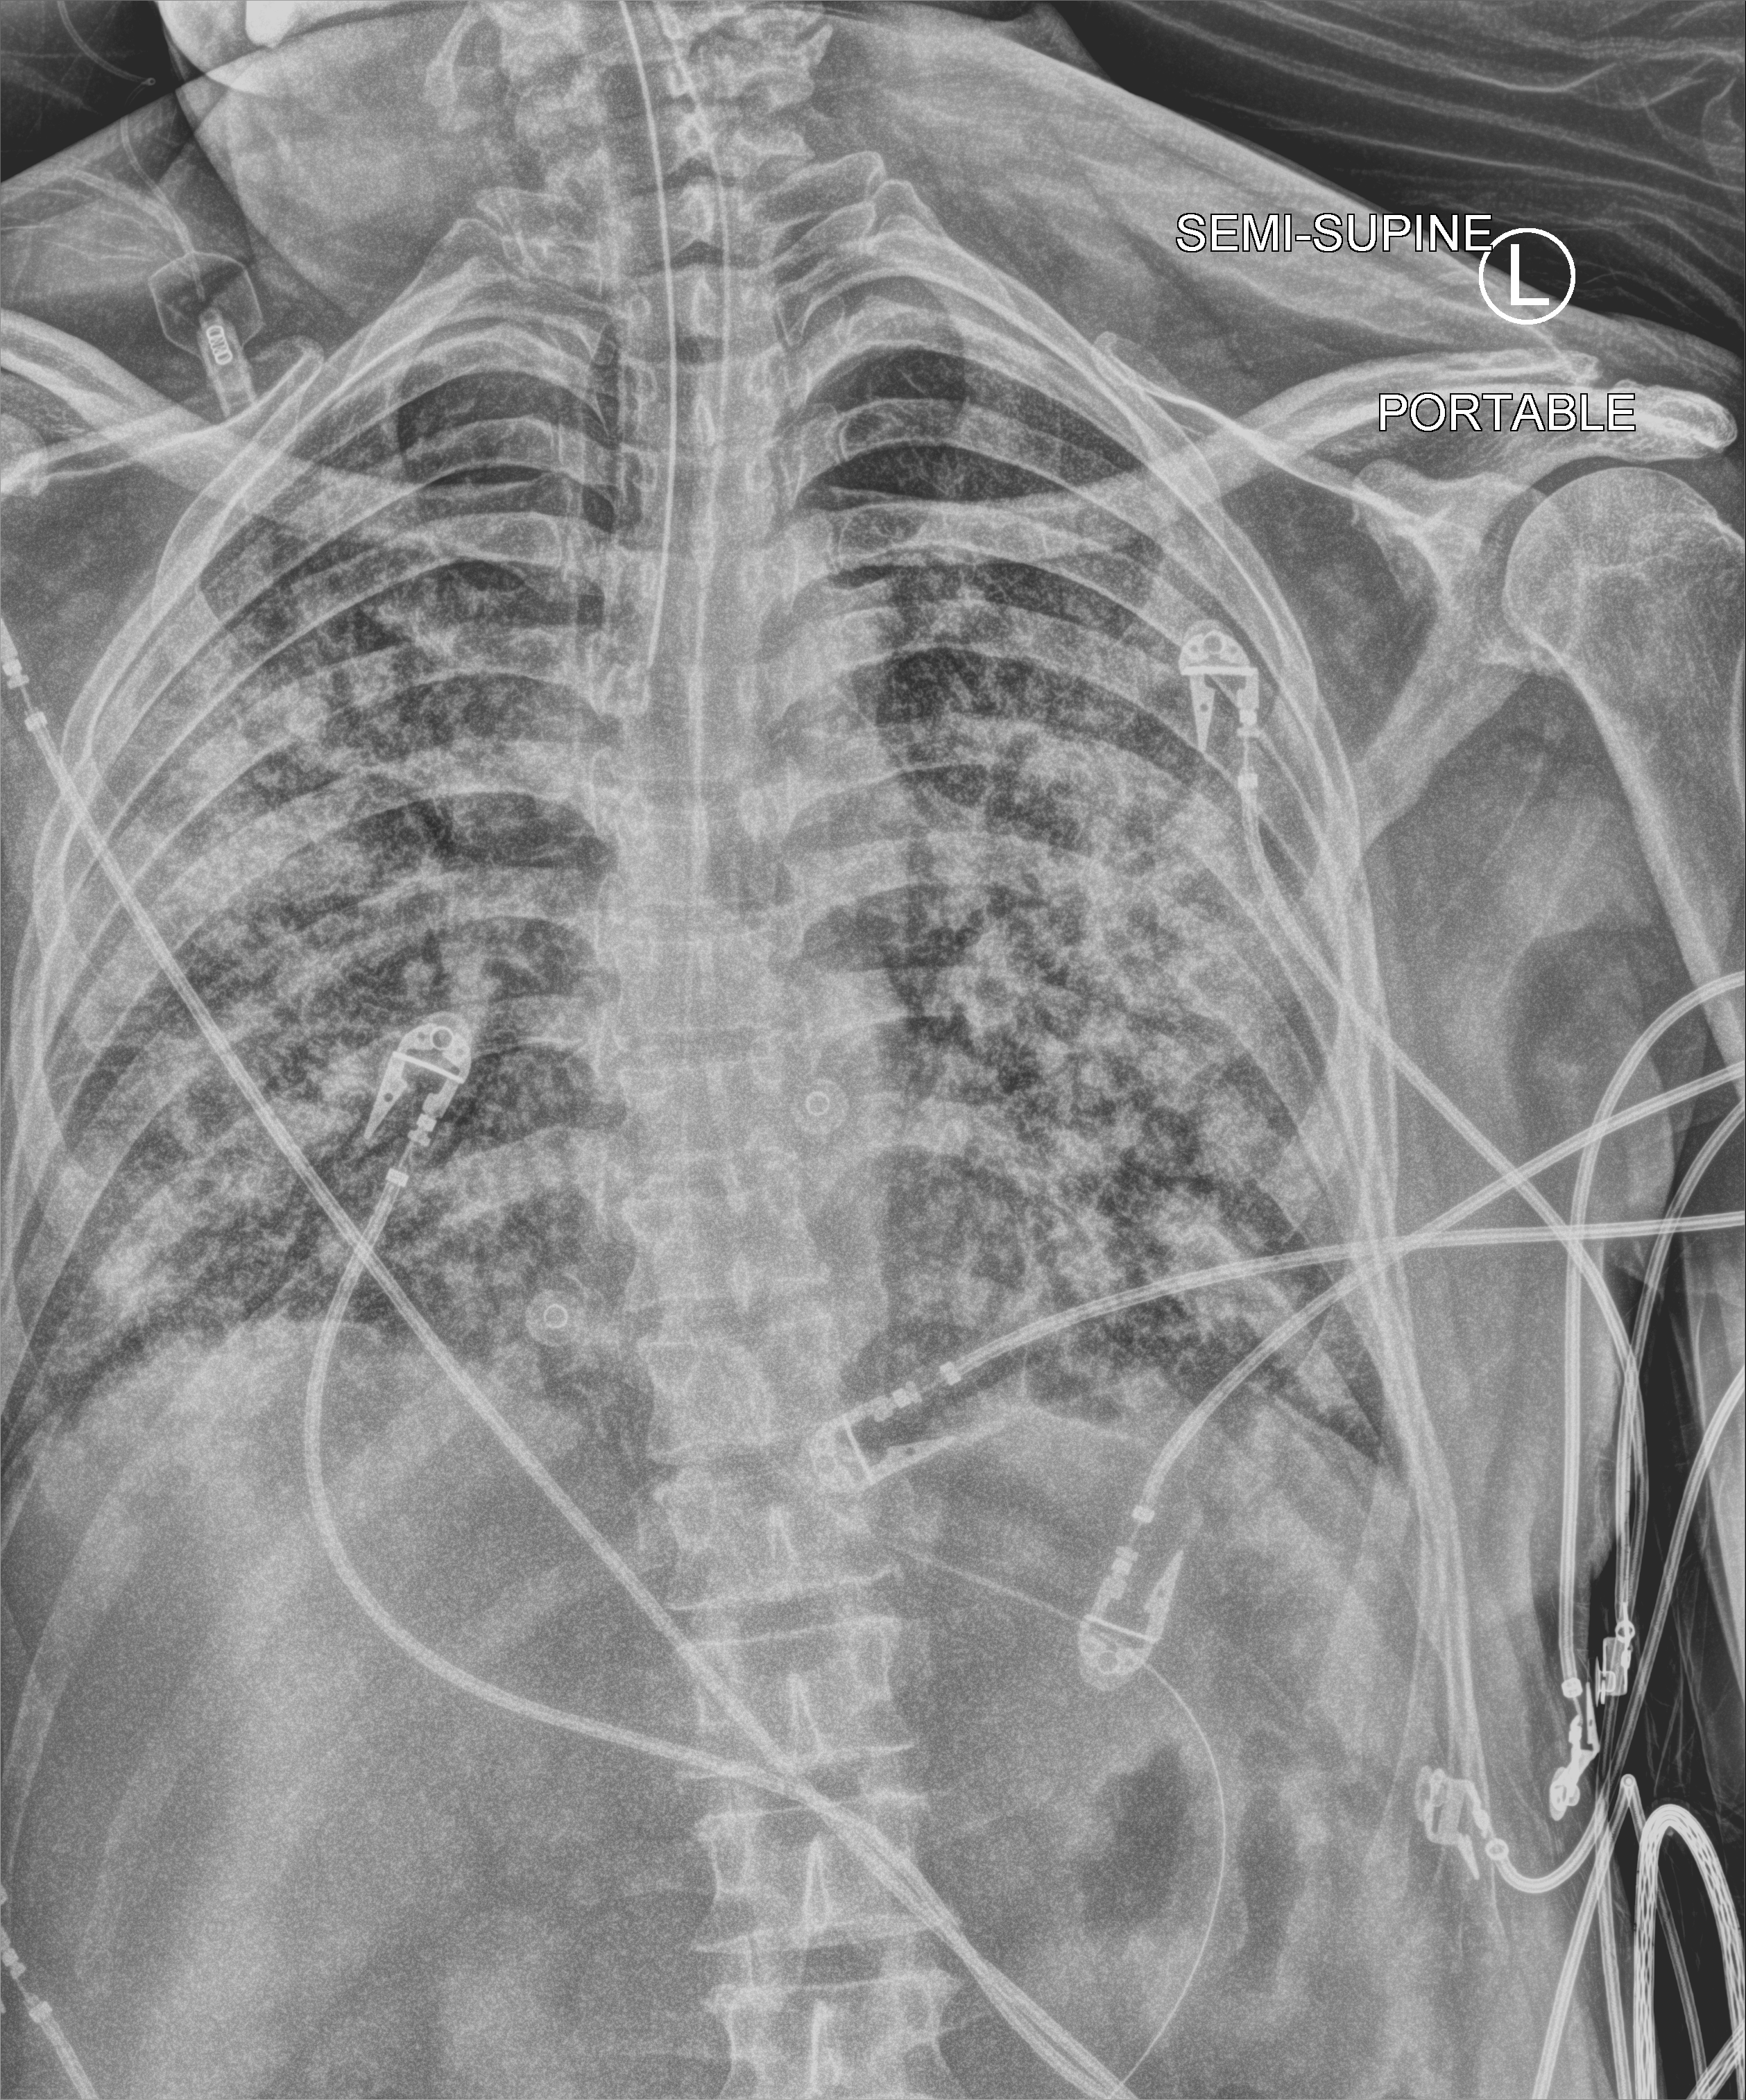
Portable chest radiograph; anteroposterior (AP) projection. Patient hospitalised with COVID-19; male, aged 60–74 years.
Hospital-stay facts (about this admission, not read from this image; timing relative to this image not recorded):
- admitted to intensive care during this hospital stay: yes
- diabetes (admission record): no